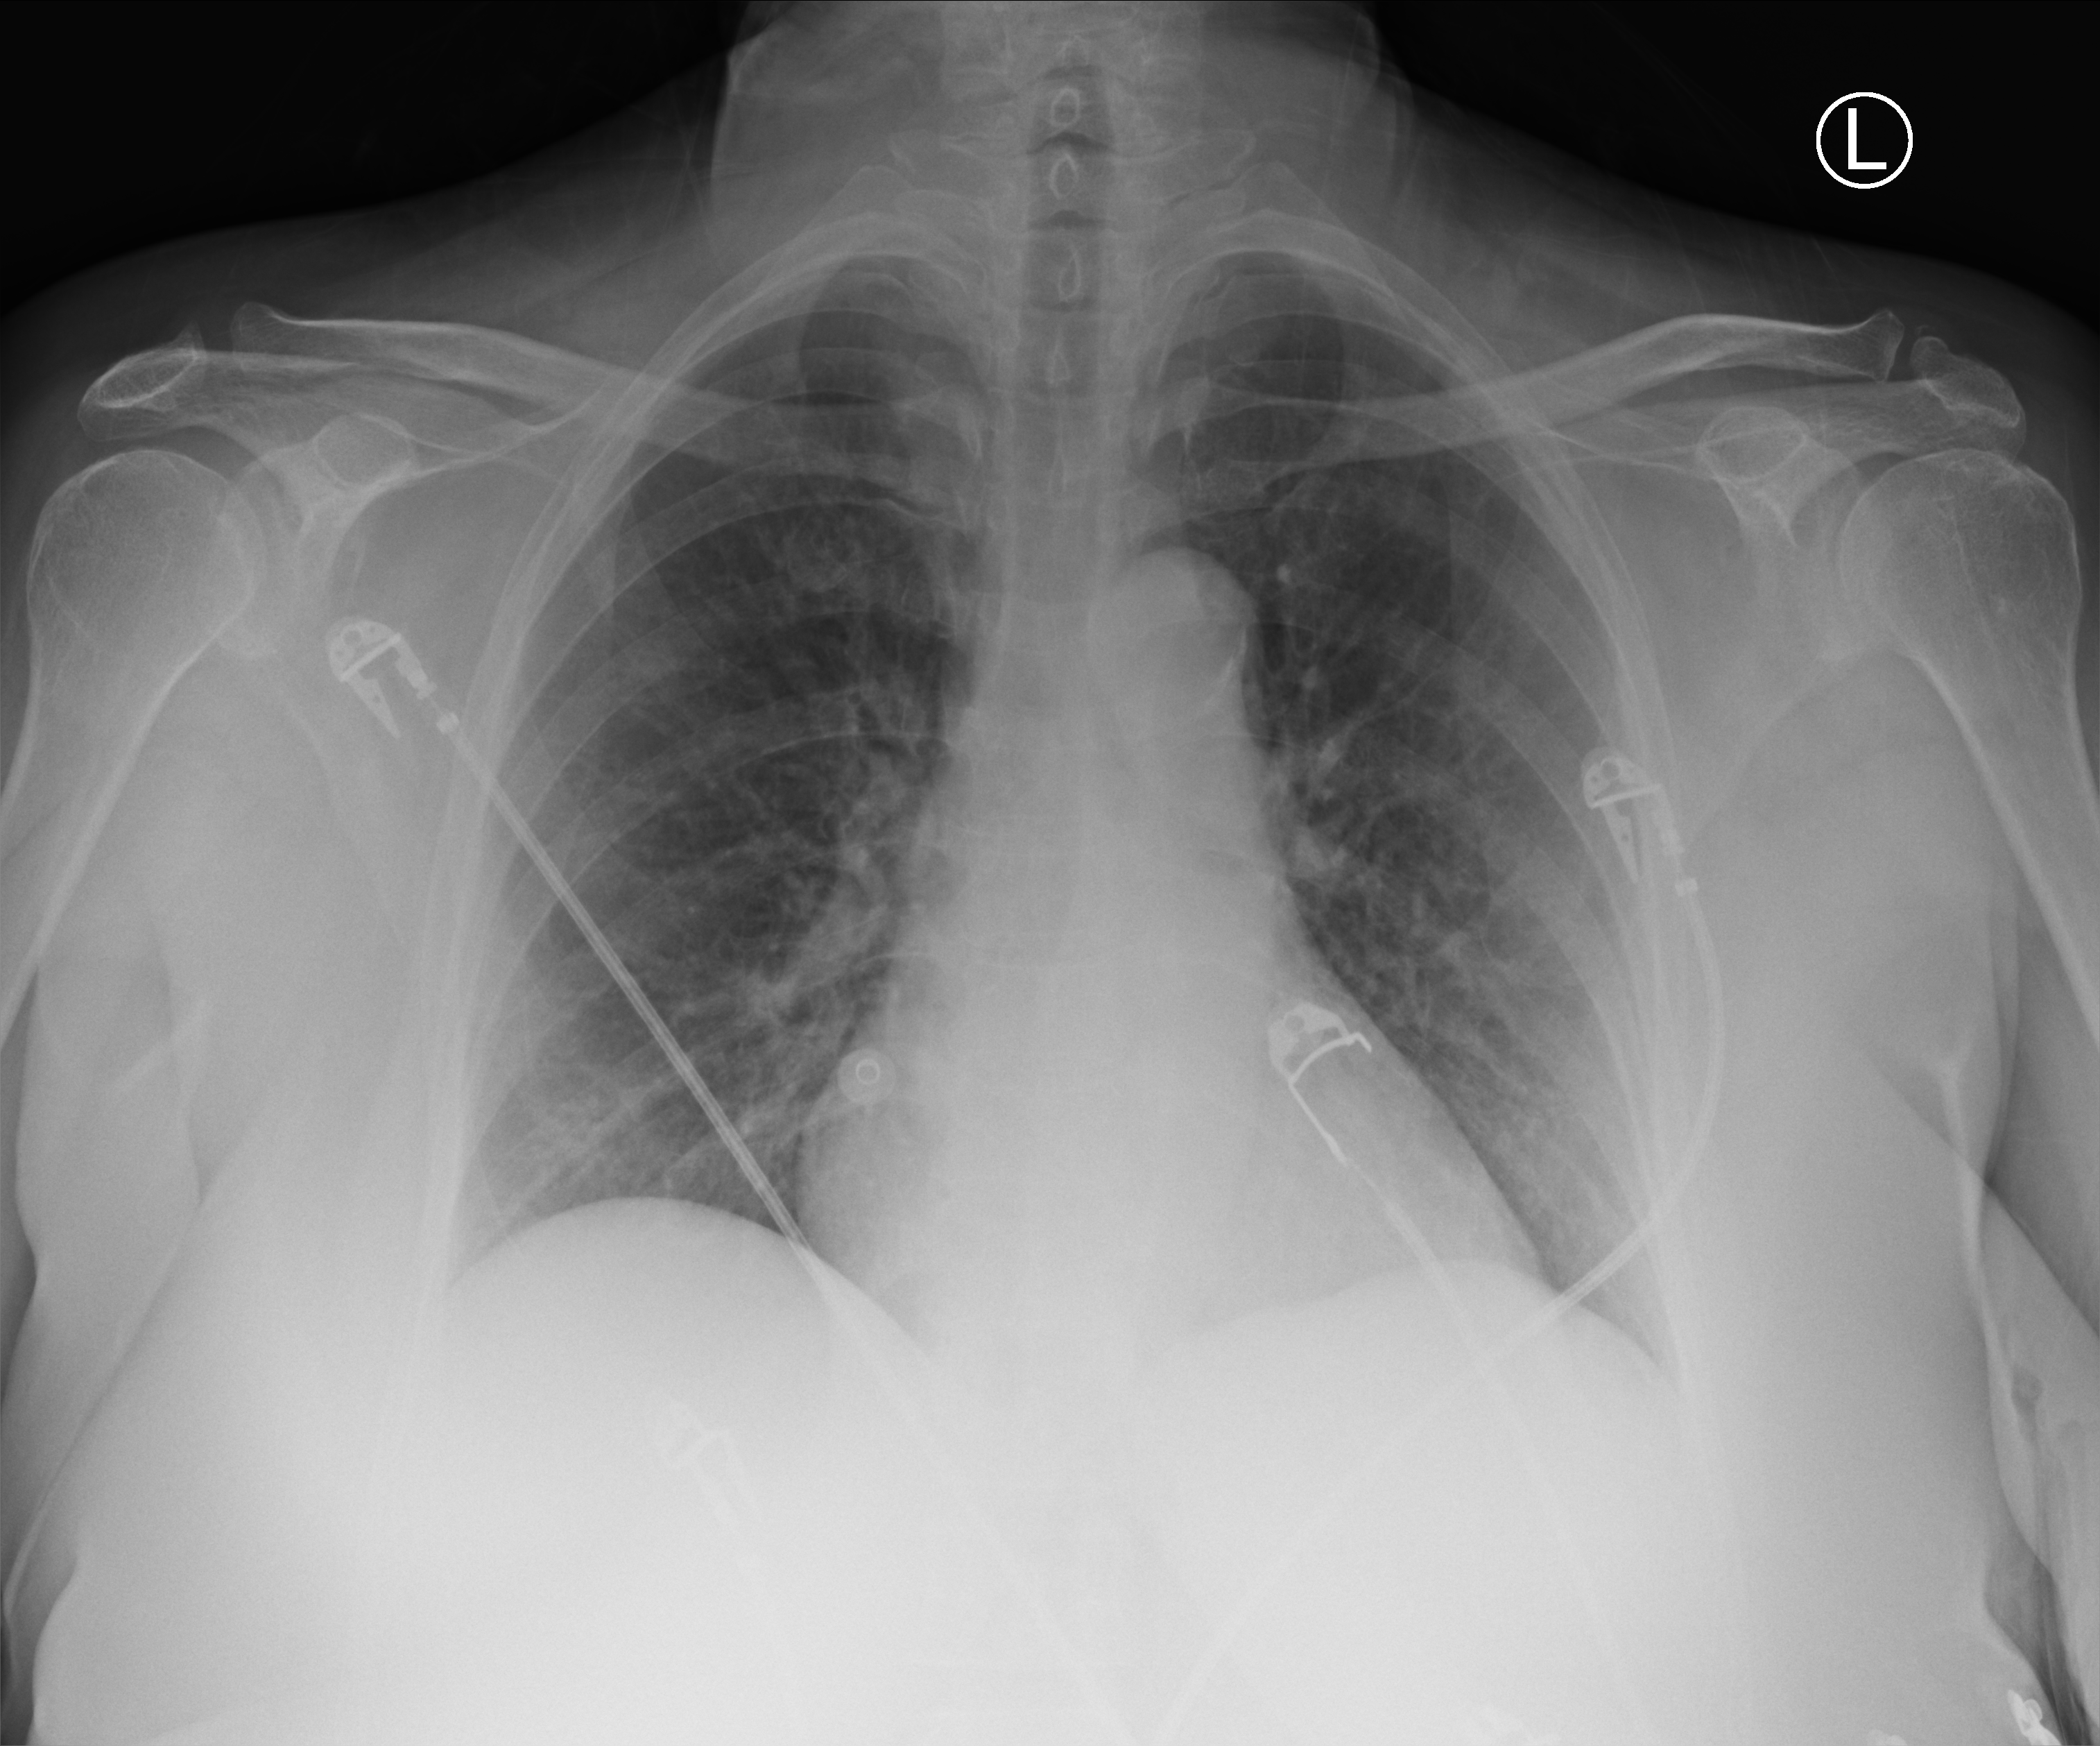
Portable chest radiograph, anteroposterior (AP) projection. Patient hospitalised with COVID-19; female, aged 60–74 years.
Admission-level facts for this patient (not findings on this image; timing relative to this image not recorded): mechanically ventilated during this hospital stay: no; admitted to intensive care during this hospital stay: no.